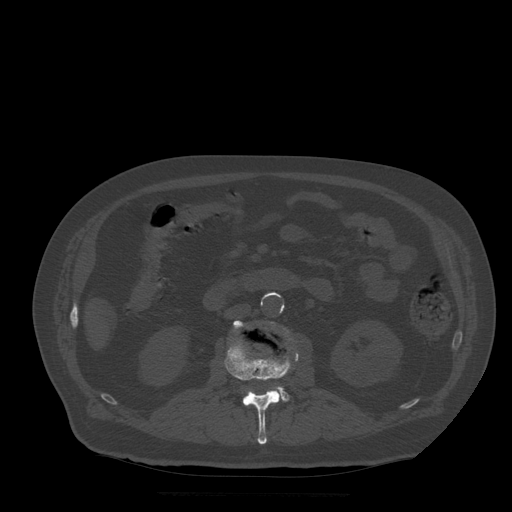
CT including the spine, one axial slice; position 161 of 522 along the scan axis; bone window (W 1800 / L 400 HU); 1.25 mm slice thickness; 512 × 512 image matrix. Patient age 72 years. Case-level facts recorded for this patient, not image findings: primary cancer: prostate.
Annotated regions visible in this slice (semi-automatic segmentation, software-assisted and operator-edited):
- L2 vertebra: bounding box (x1, y1, x2, y2) in pixels: (225, 341, 299, 445)
- L3 vertebra: (233, 321, 289, 401)